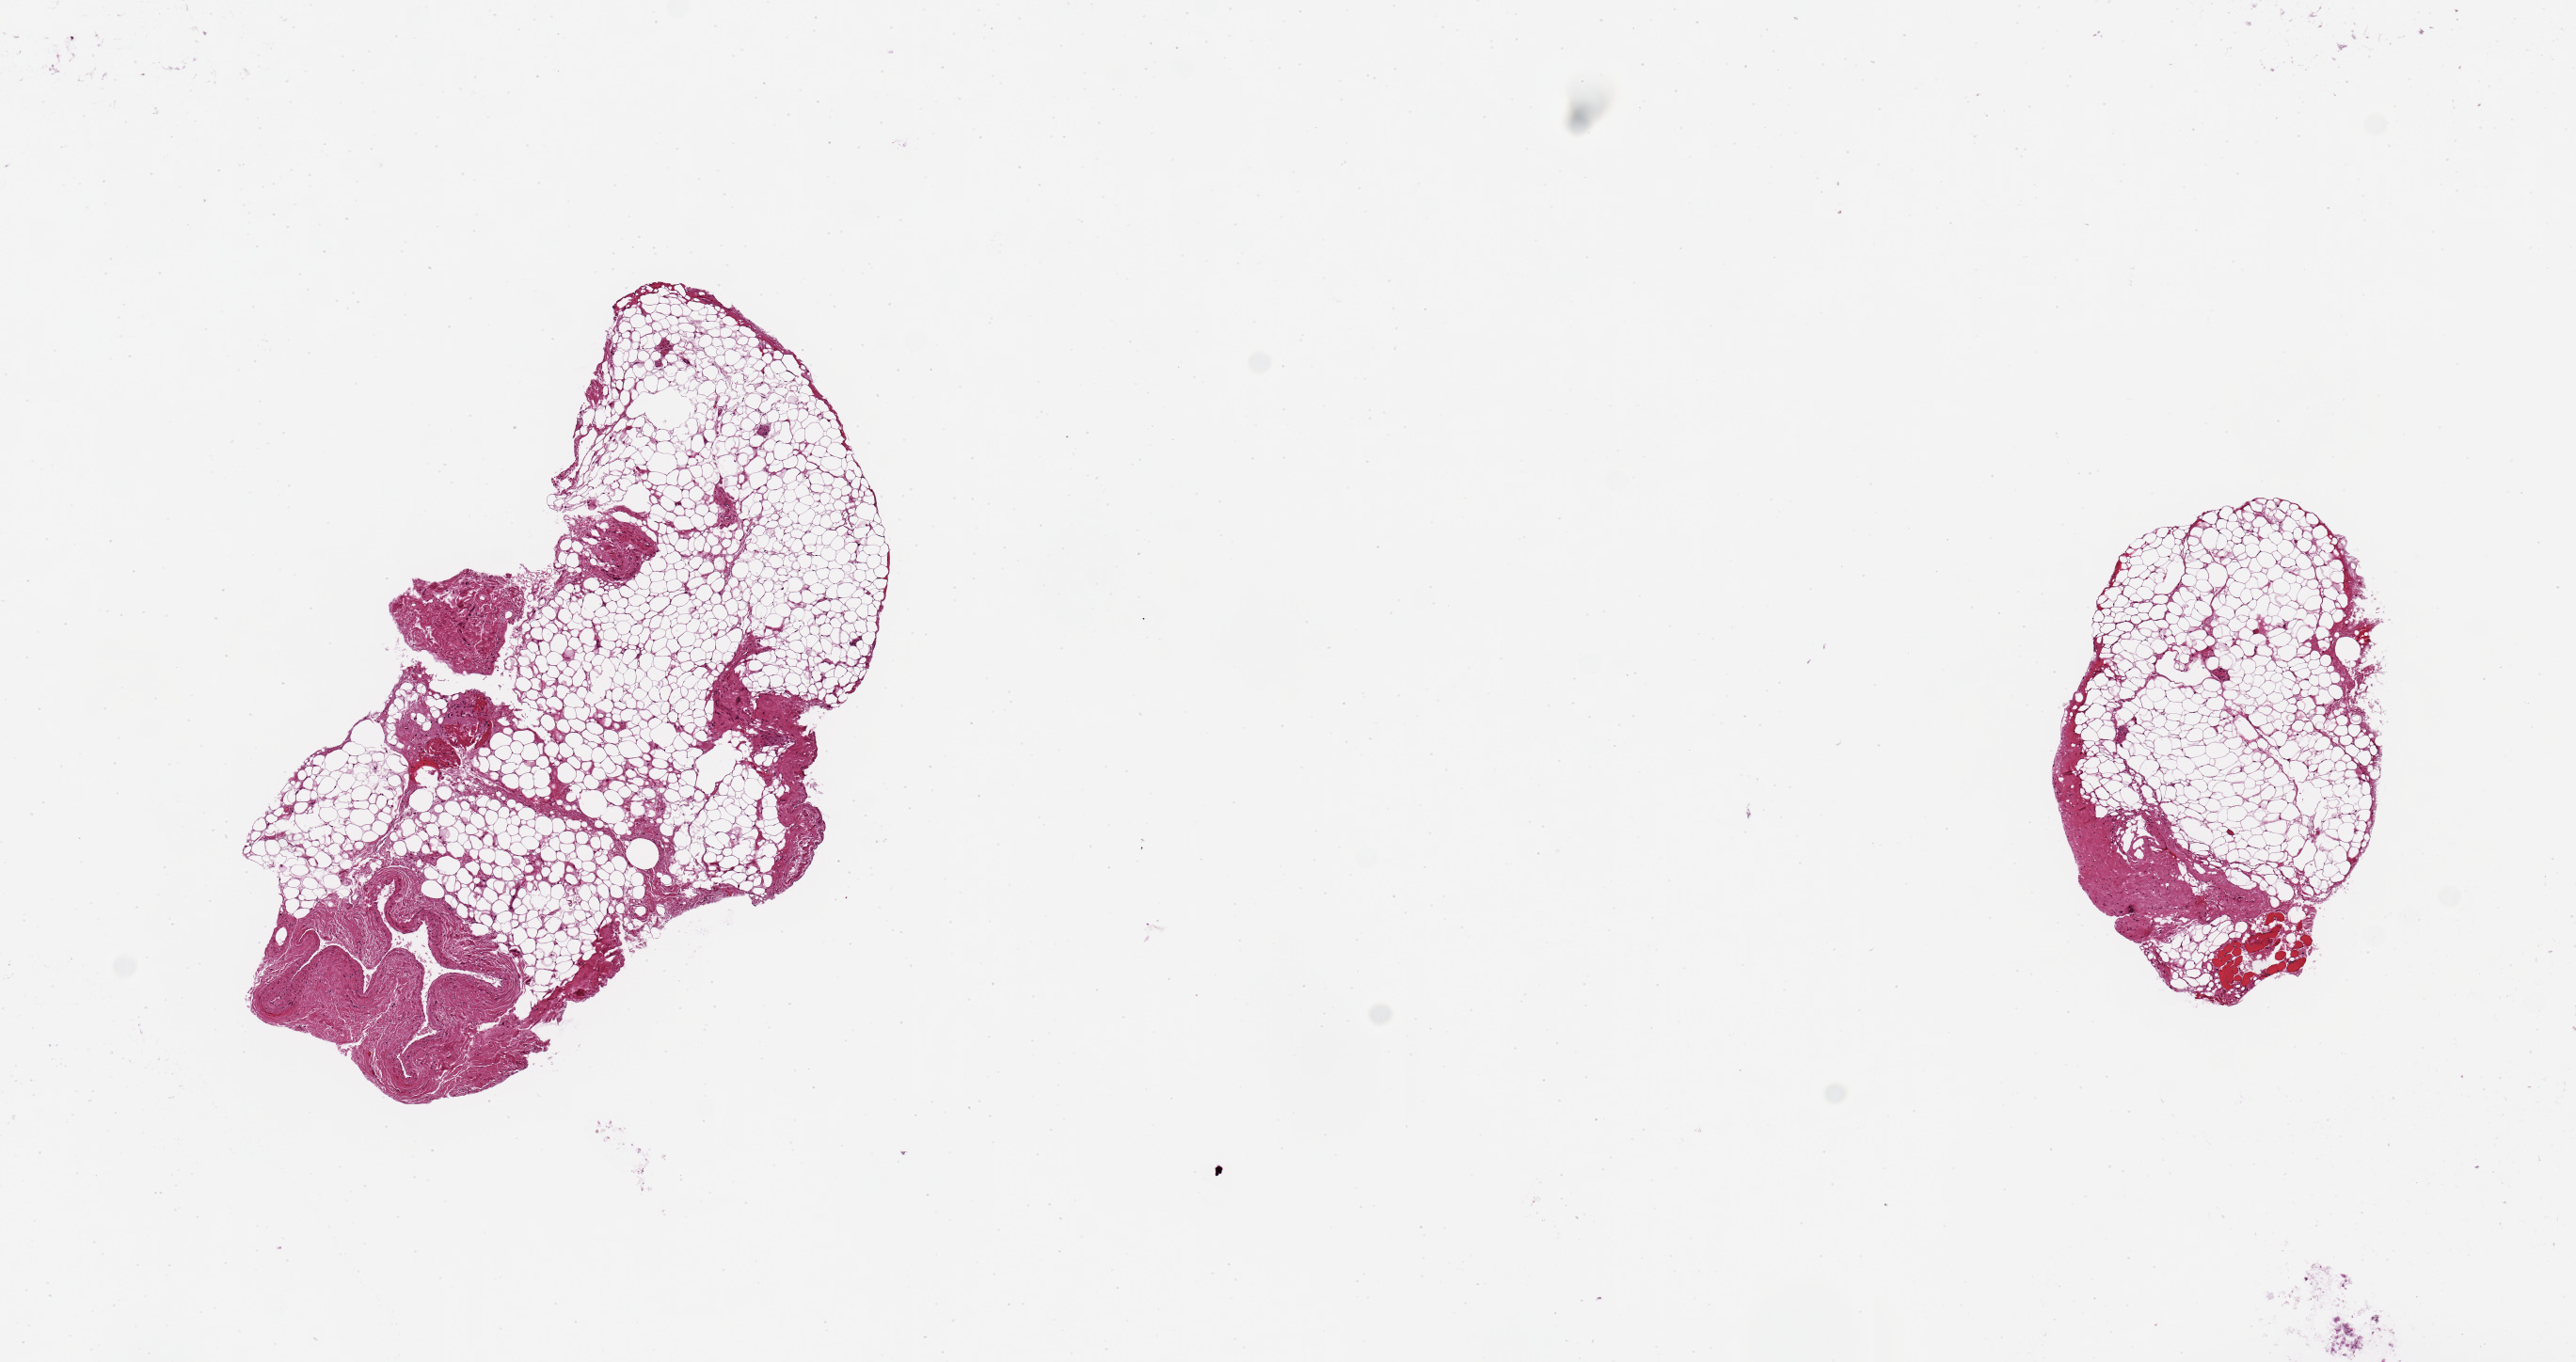
Haematoxylin and eosin whole-slide image — a low-resolution overview of the entire scanned area, about 10.8 x 5.7 mm; PAXgene-fixed, paraffin-embedded tissue; target tissue: coronary artery; donor tissue sample. Donor sex: male.
Pathologist's review note for this sample: 2 aliquots, ~3.2mm. One is all fat, the other is ~90% fat with ~0.8mm vessel on edge of one aliquot.